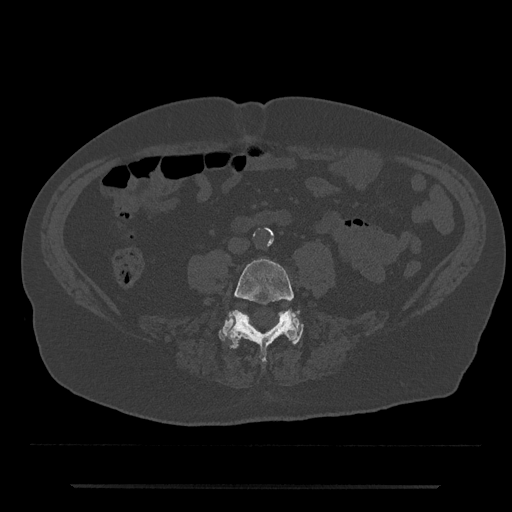
CT including the spine, one axial slice. Position 341 of 797 along the scan axis. Bone window (W 1800 / L 400 HU). 0.5 mm slice thickness. 512 × 512 image matrix. Male patient, age 80 years. Case-level facts recorded for this patient, not image findings: primary cancer: prostate; vertebrae with lytic lesions (as recorded): L1, T11.
Outlined on this slice (semi-automatically segmented with operator editing):
- L4 vertebra: bounding box (x1, y1, x2, y2) in pixels: (228, 258, 300, 362)
- L5 vertebra: (219, 312, 303, 345)